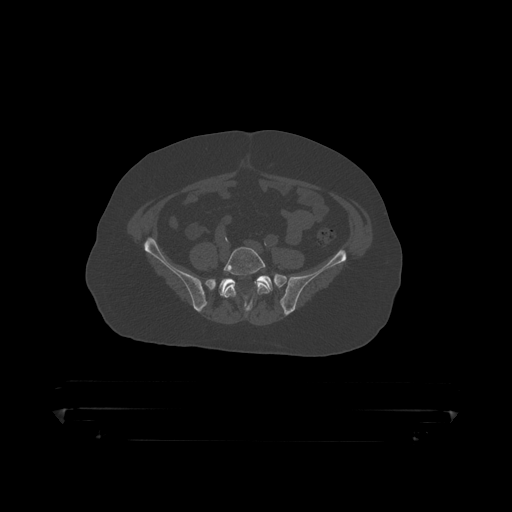
CT including the spine, one axial slice. Position 33 of 390 along the scan axis. Bone window (W 1800 / L 400 HU). 1.25 mm slice thickness. 512 × 512 image matrix, field of view 650 × 650 mm. Male patient, age 60 years. From the clinical record (not read from this slice): primary cancer: prostate.
Outlined on this slice (semi-automatically segmented with operator editing):
- L5 vertebra: bounding box [x1, y1, x2, y2] px = [223, 247, 270, 311]